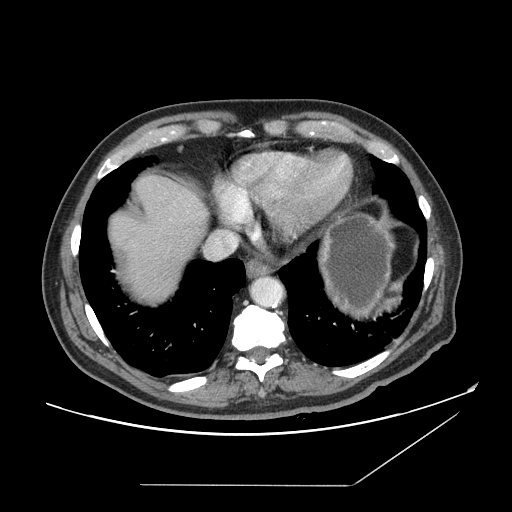
Contrast-enhanced abdominal CT, one axial slice. Slice 139 of 166 in the series (ordered by position). 120 kVp. Intravenous contrast given. Soft-tissue window (W 400 / L 40 HU). 2.5 mm slice thickness. 512 × 512 image matrix, field of view 416 × 416 mm. Male patient, age 80 years. From the clinical record (not read from this slice): diagnosis: colorectal cancer liver metastases, imaged before liver resection; multiple liver metastases: no; largest metastasis: 2.2 cm; chemotherapy before resection: no.
Outlined on this slice (manually delineated by an expert):
- liver: bounding box <107,175,210,304> (left, top, right, bottom; pixels)
- planned liver remnant (the part of the liver to remain after resection): <107,175,210,257>